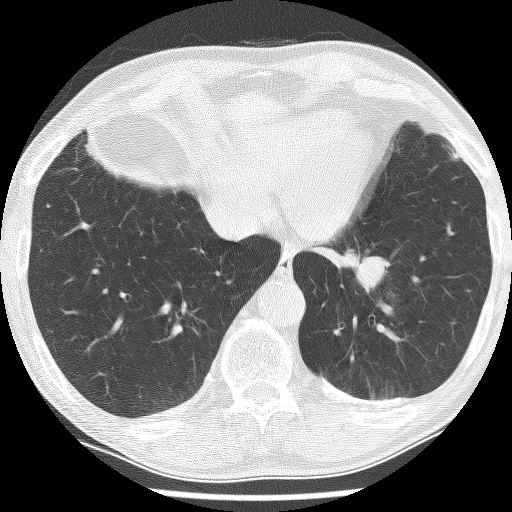
Axial slice from a low-dose chest CT screening exam, baseline screening round, lung window (W 1500 / L -600 HU), 2.5 mm slice thickness, lung (sharp) reconstruction kernel (BONE), slice 185 of 226 in the series, 512 × 512 image matrix. Male, age 74 years at enrolment. Current smoker at enrolment.
- Expert reader's lesion annotation, bounding box (x1, y1, x2, y2) in pixels: (312, 215, 412, 307).
- The exam's reader record, not a measurement of the box and not confirmed to be the same lesion: non-calcified nodule or mass ≥4 mm, left lower lobe, 30 × 27 mm, spiculated (stellate) margins, soft tissue attenuation.
- Later outcome: lung cancer diagnosed 151 days after this screen — adenocarcinoma, NOS, left lower lobe, stage IIIA (AJCC 6th edition), 49 mm at pathology.